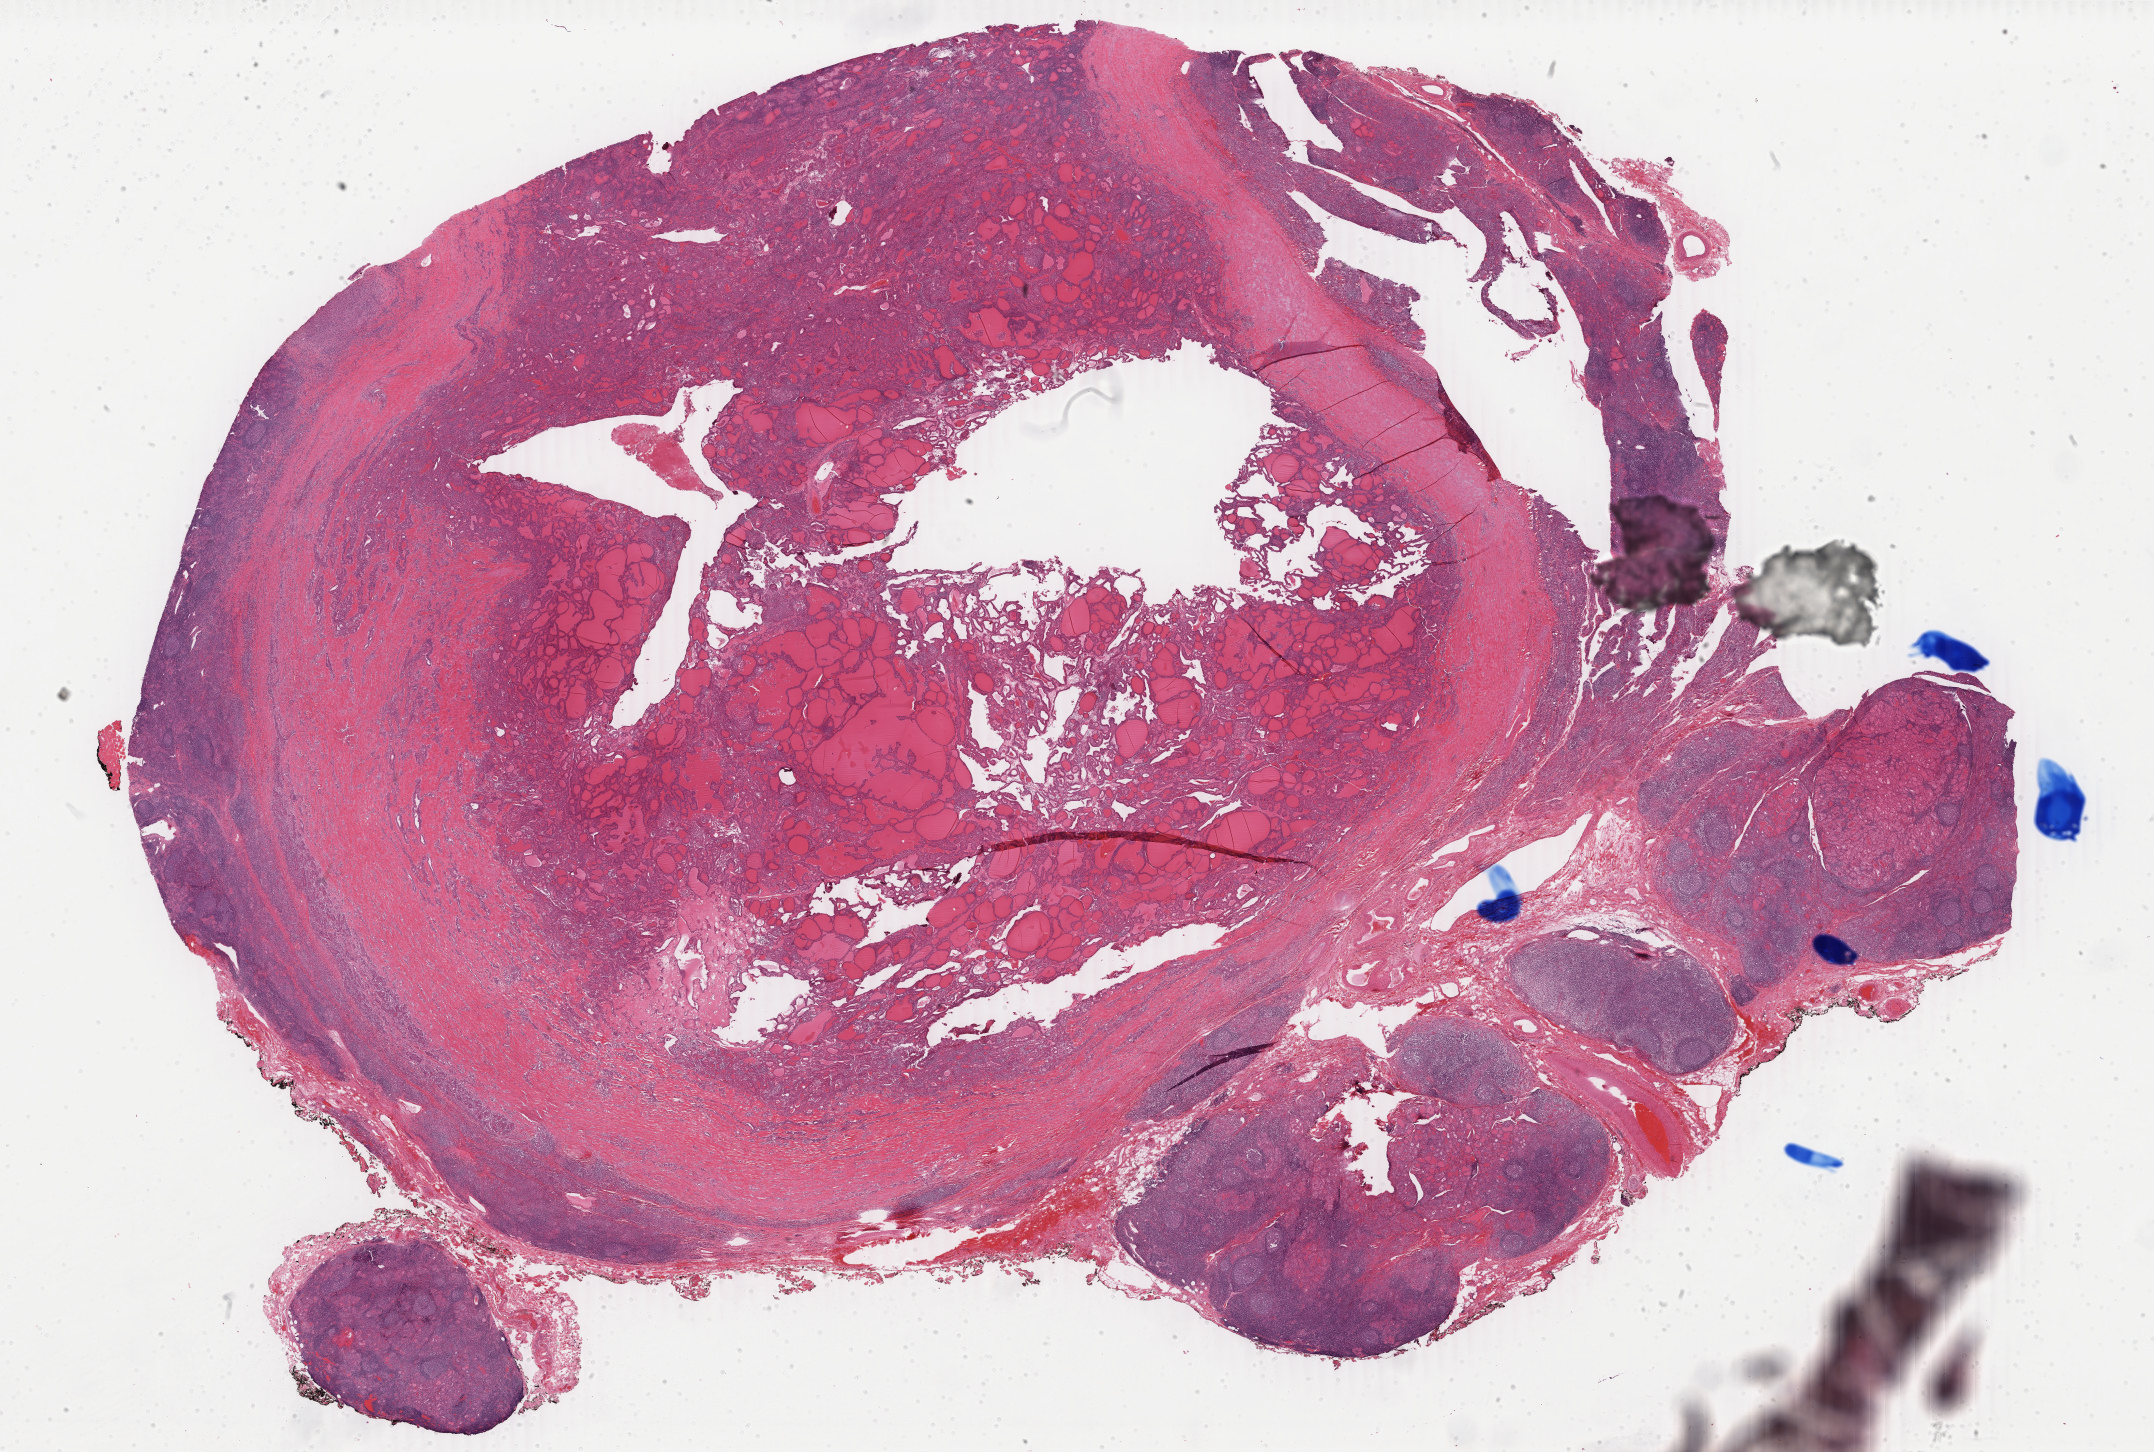
Whole-slide histology image, H&E-stained, whole scanned area (about 34.3 x 23.1 mm, slide scanned at 40x) shown as a low-resolution overview, formalin-fixed paraffin-embedded (FFPE) diagnostic section, sample: primary tumour, thyroid. Female, age 32 years at initial diagnosis.
• AJCC pathologic stage: I (7th edition)
• lymph nodes positive (case pathology): 0 of 4 examined
• pathologic diagnosis: Papillary adenocarcinoma, NOS